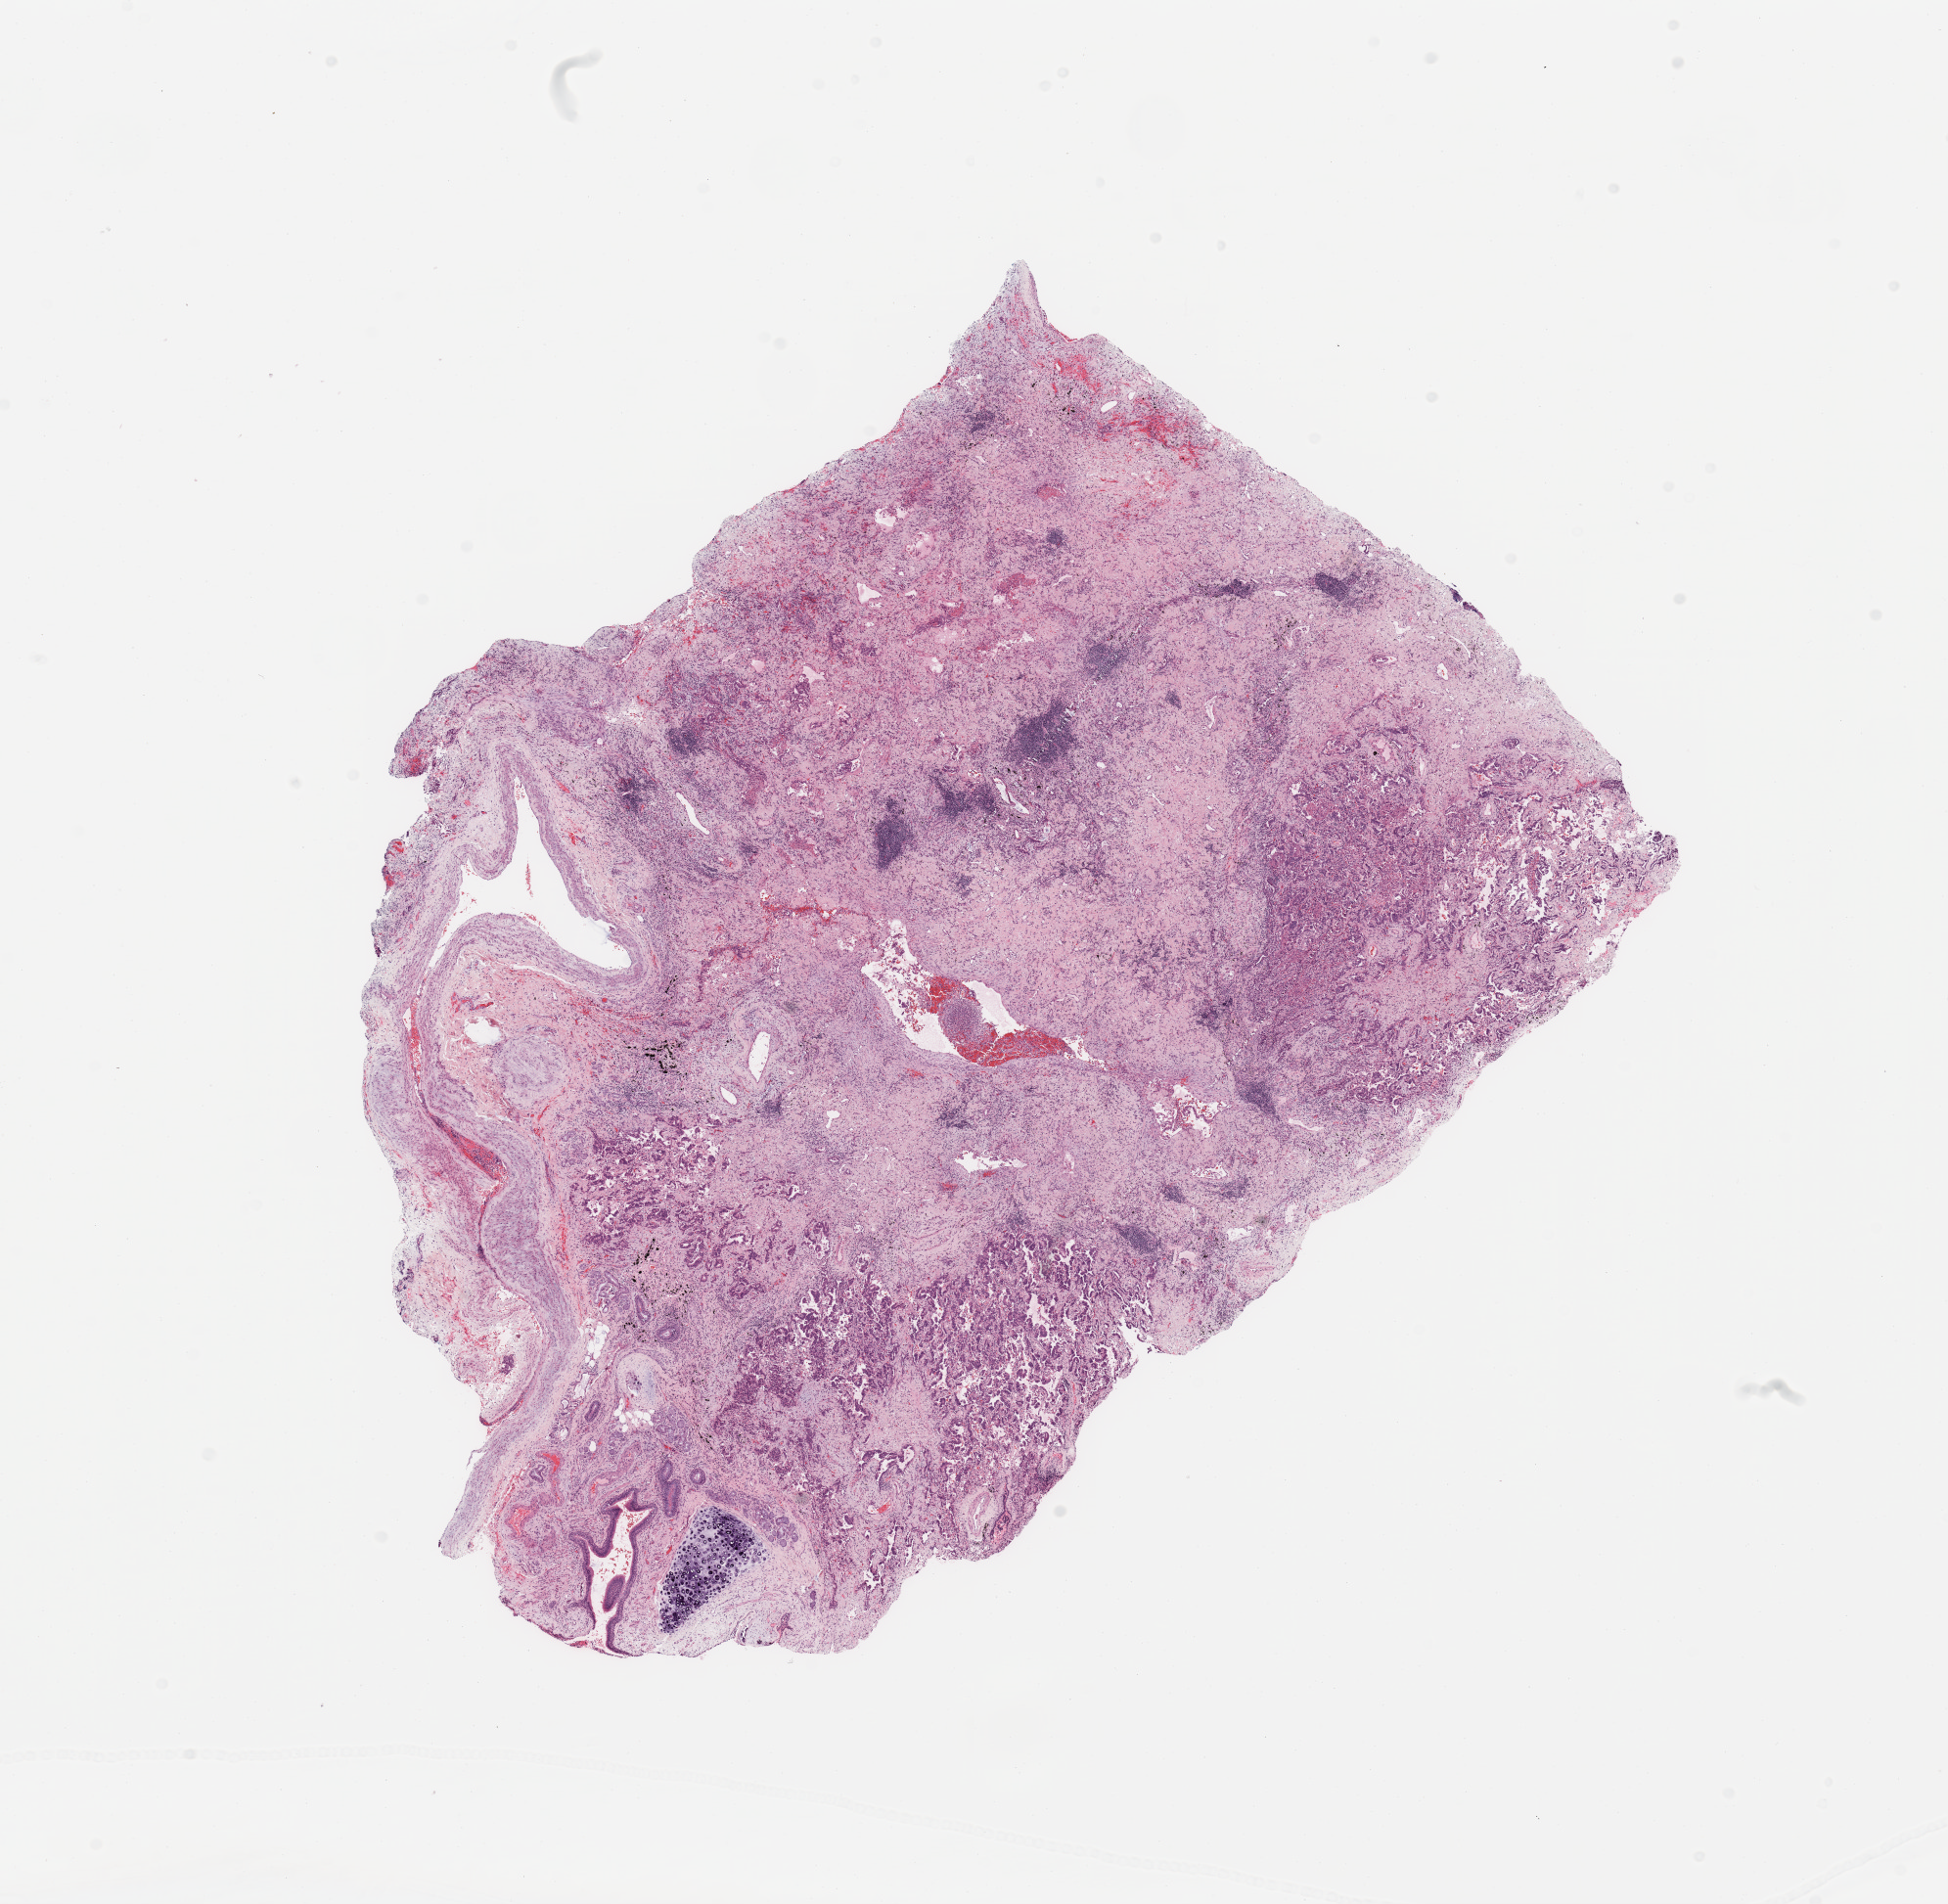
Digitized H&E-stained tissue section (whole slide), a low-resolution overview of the entire scanned area, about 15.8 x 15.4 mm (from a 20x scan); tumour tissue sample, sampled site: lung. 71-year-old male patient. Histologic grade: G2 (moderately differentiated). Composition of this section per pathologist review: tumour nuclei 60%, necrosis 5%.
• primary tumour site (as recorded): right upper lobe
• histologic diagnosis: Adenocarcinoma, NOS
• AJCC pathologic stage: IB